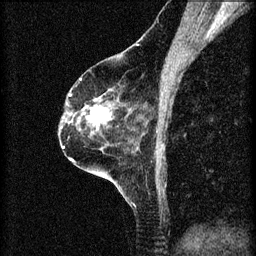
Breast MRI (dynamic contrast-enhanced), one sagittal slice. Position 40 of 60 along the scan axis. 3 images stored at this slice position (order not interpretable as contrast timing). 1.5 T. TE 4.2 ms, TR 8.2 ms. 2 mm slice thickness. 256 × 256 image matrix, field of view 180 × 180 mm. Female patient, age 60 years.
Structures marked on this image (semi-automatic segmentation, software-assisted and operator-edited):
- analysis volume of interest (the breast-tissue region the enhancement analysis was run in; not a lesion): bounding box (x1, y1, x2, y2) in pixels: (78, 96, 113, 131)
- tumour enhancement mask (voxels above the 70 % enhancement threshold inside the analysis volume of interest): (81, 98, 112, 125)